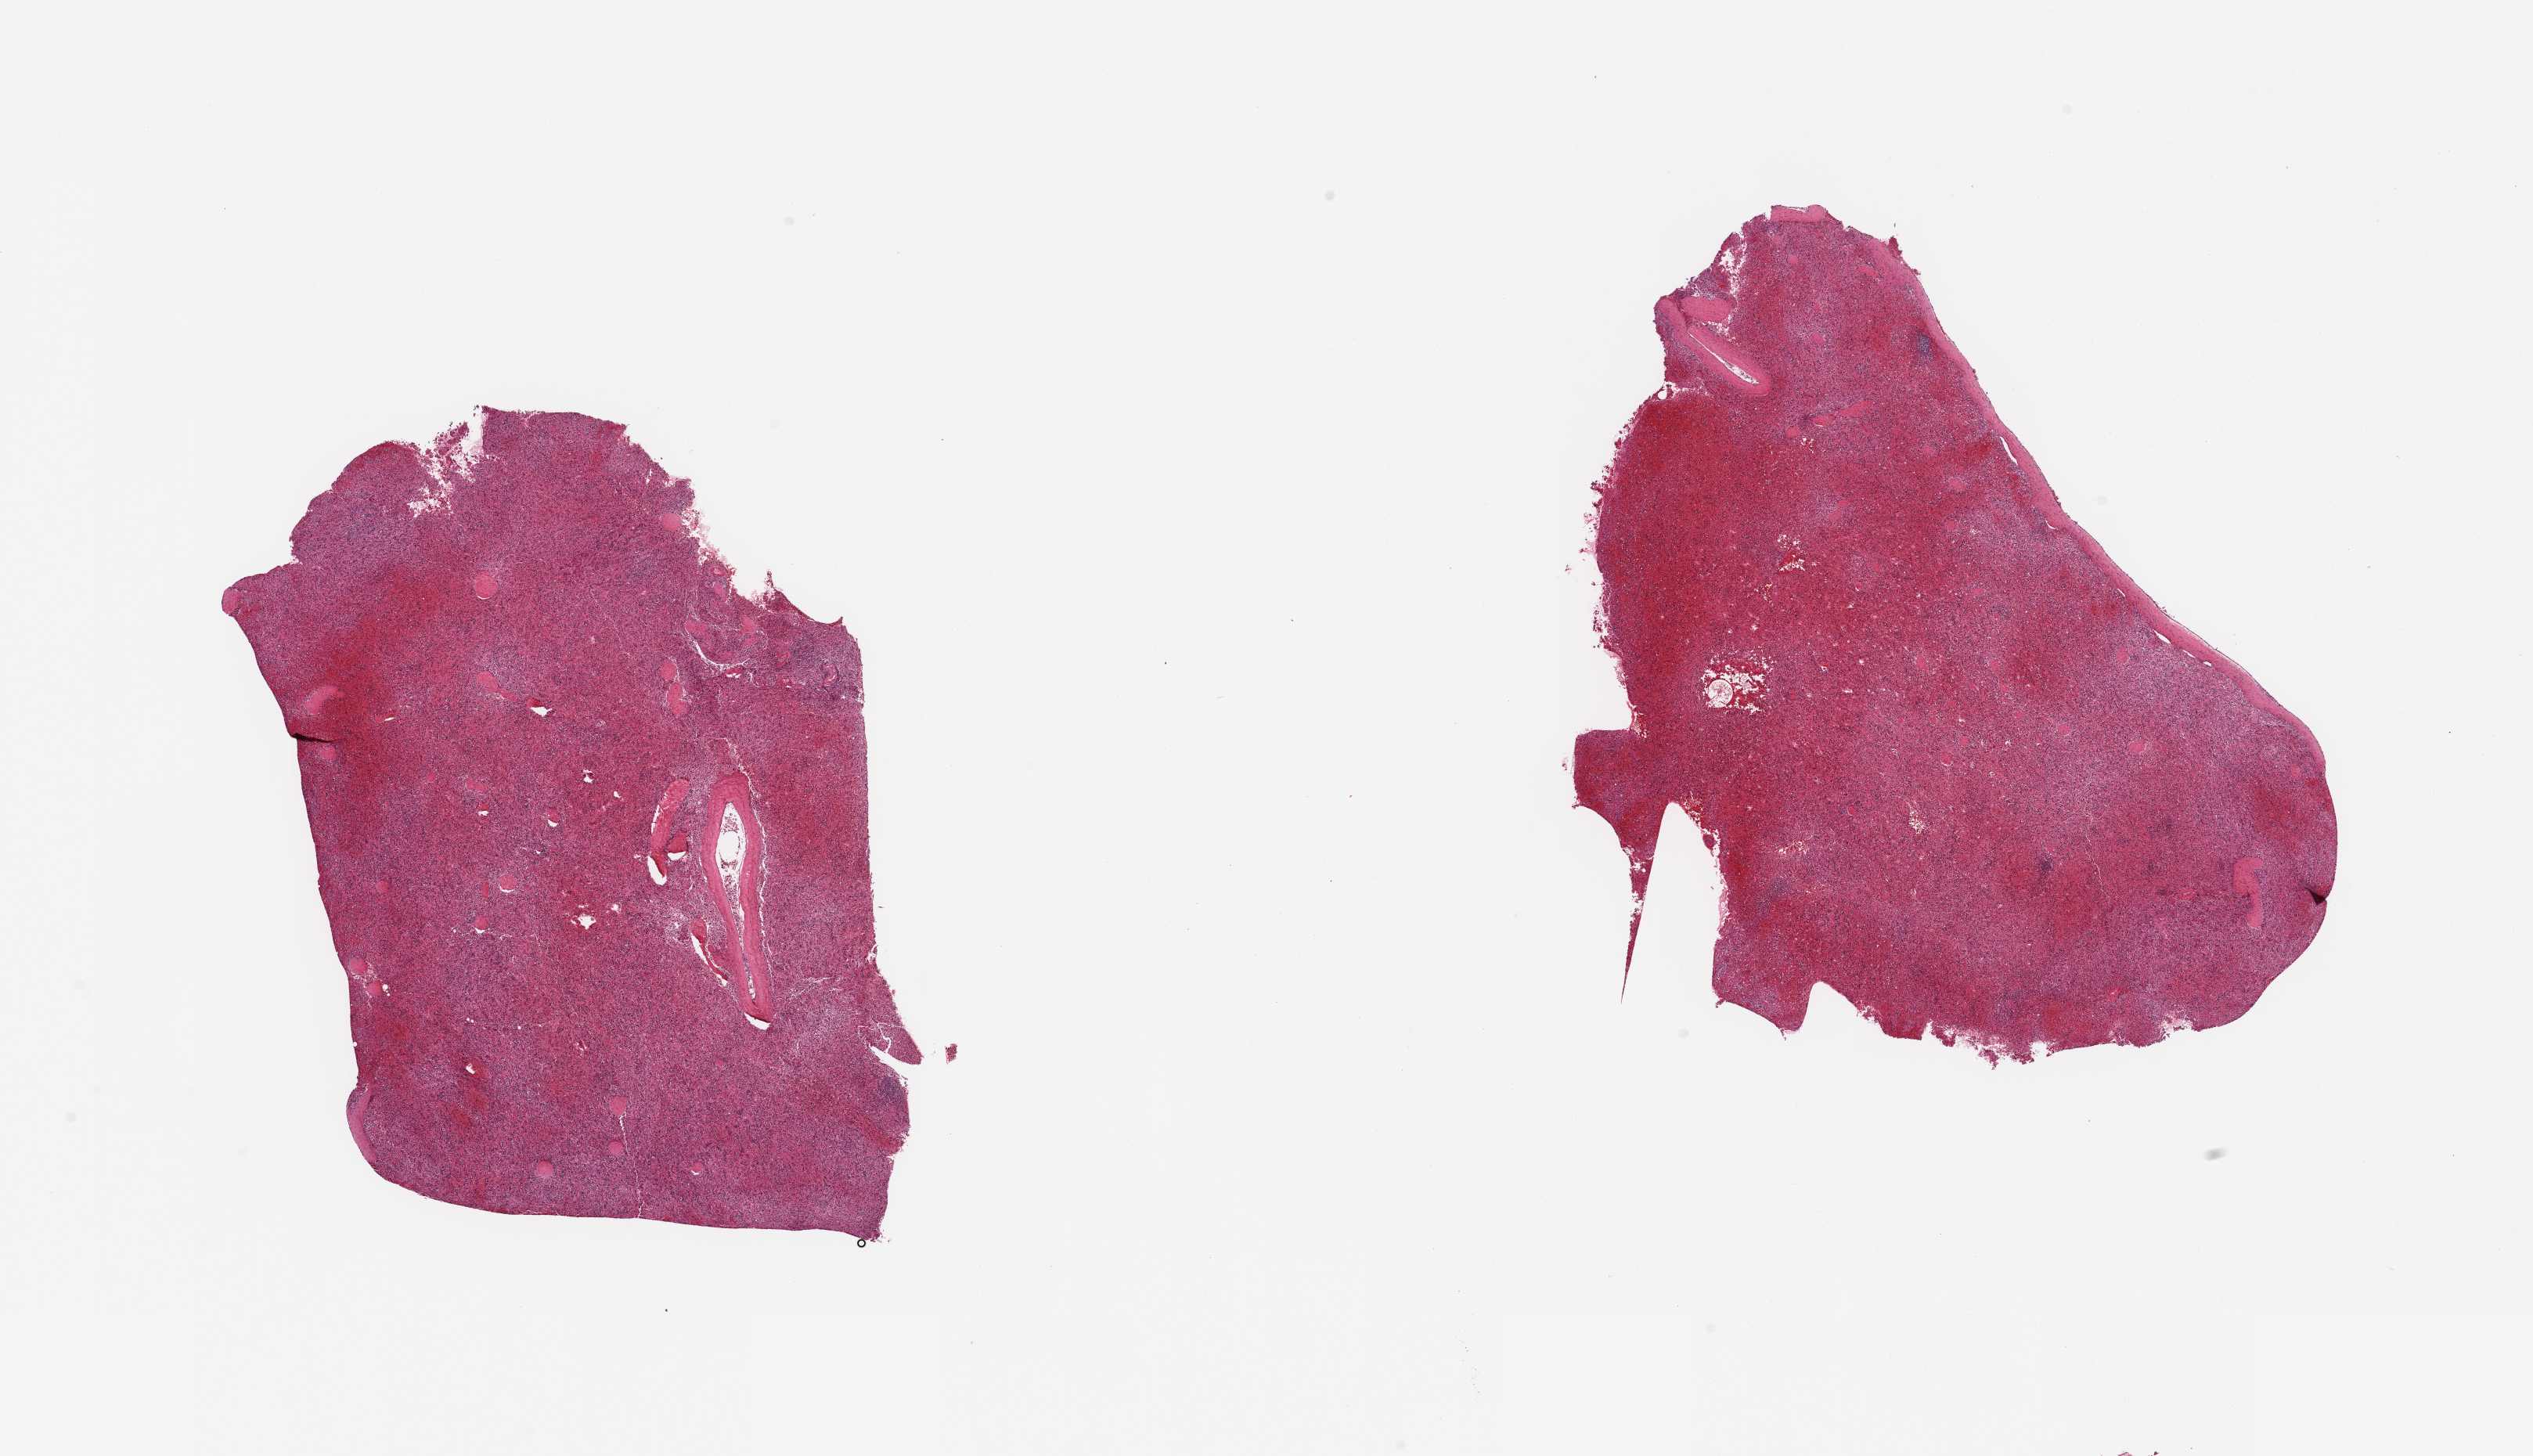
Digitized haematoxylin and eosin-stained section, low-resolution overview of the scanned area, about 25.6 x 14.7 mm (slide scanned at 20x), PAXgene-fixed paraffin-embedded (PFPE) section, section of spleen (target tissue), tissue donor sample. Male donor.
- pathologist's review note for this sample: 2 pieces; moderately congested; capsule included in 1 piece